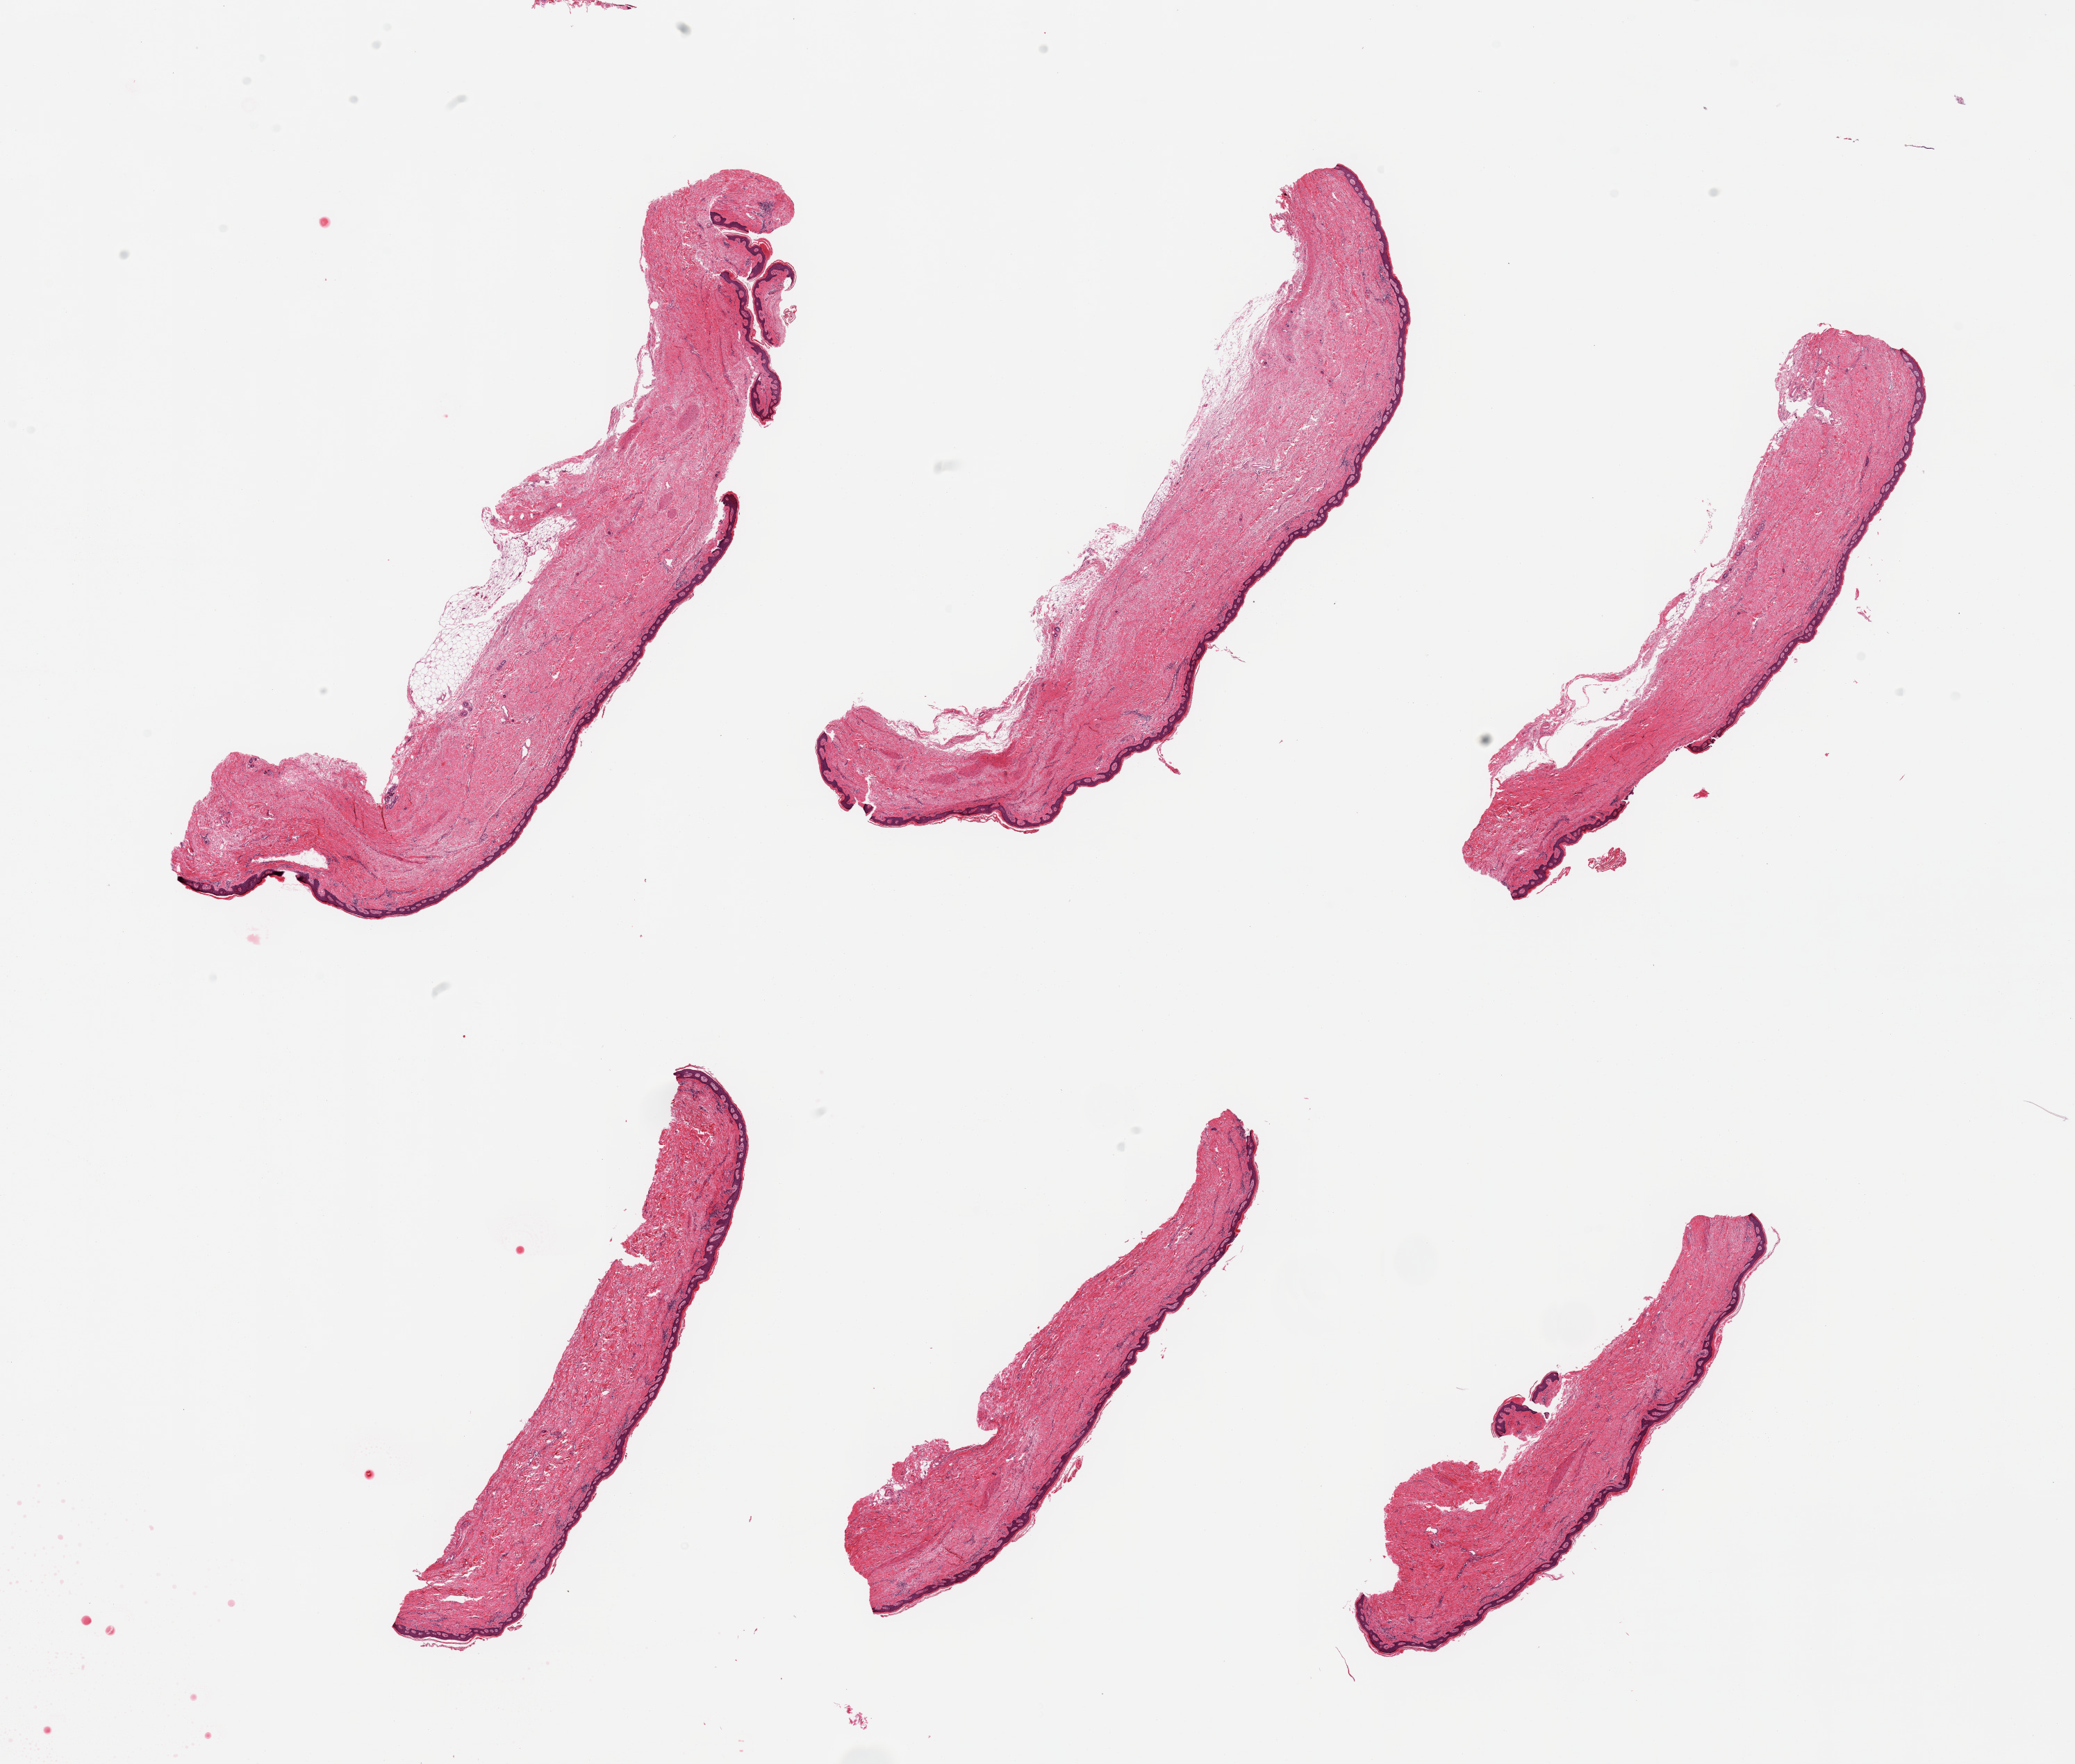
Digitized H&E-stained section, brightfield, whole scanned area (about 23.6 x 20.1 mm, acquisition: 20x scan) shown as a low-resolution overview; PAXgene-fixed, paraffin-embedded tissue; section of skin of suprapubic region (target tissue); tissue donor sample. Donor: female.
- review note (as recorded): 6 pieces; essentially well trimmed